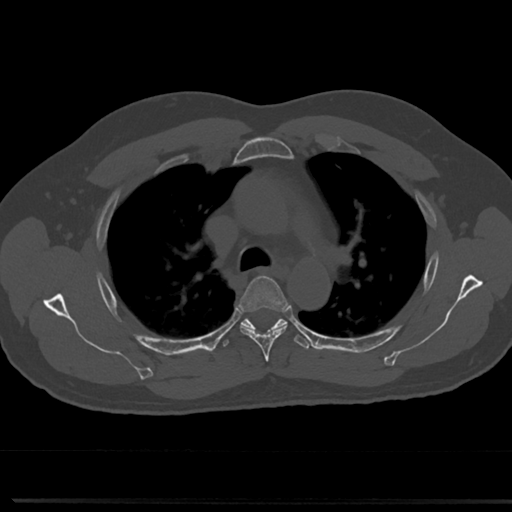
CT including the spine, one axial slice; position 529 of 817 along the scan axis; 120 kVp; bone window (W 1800 / L 400 HU); 0.5 mm slice thickness; 512 × 512 image matrix. Patient: male, 61 years. From the clinical record (not read from this slice): primary cancer: prostate.
Outlined on this slice (semi-automatic segmentation, software-assisted and operator-edited):
- T4 vertebra: box from (x=239, y=276) to (x=289, y=357) px
- T5 vertebra: (x=243, y=320)–(x=285, y=328)